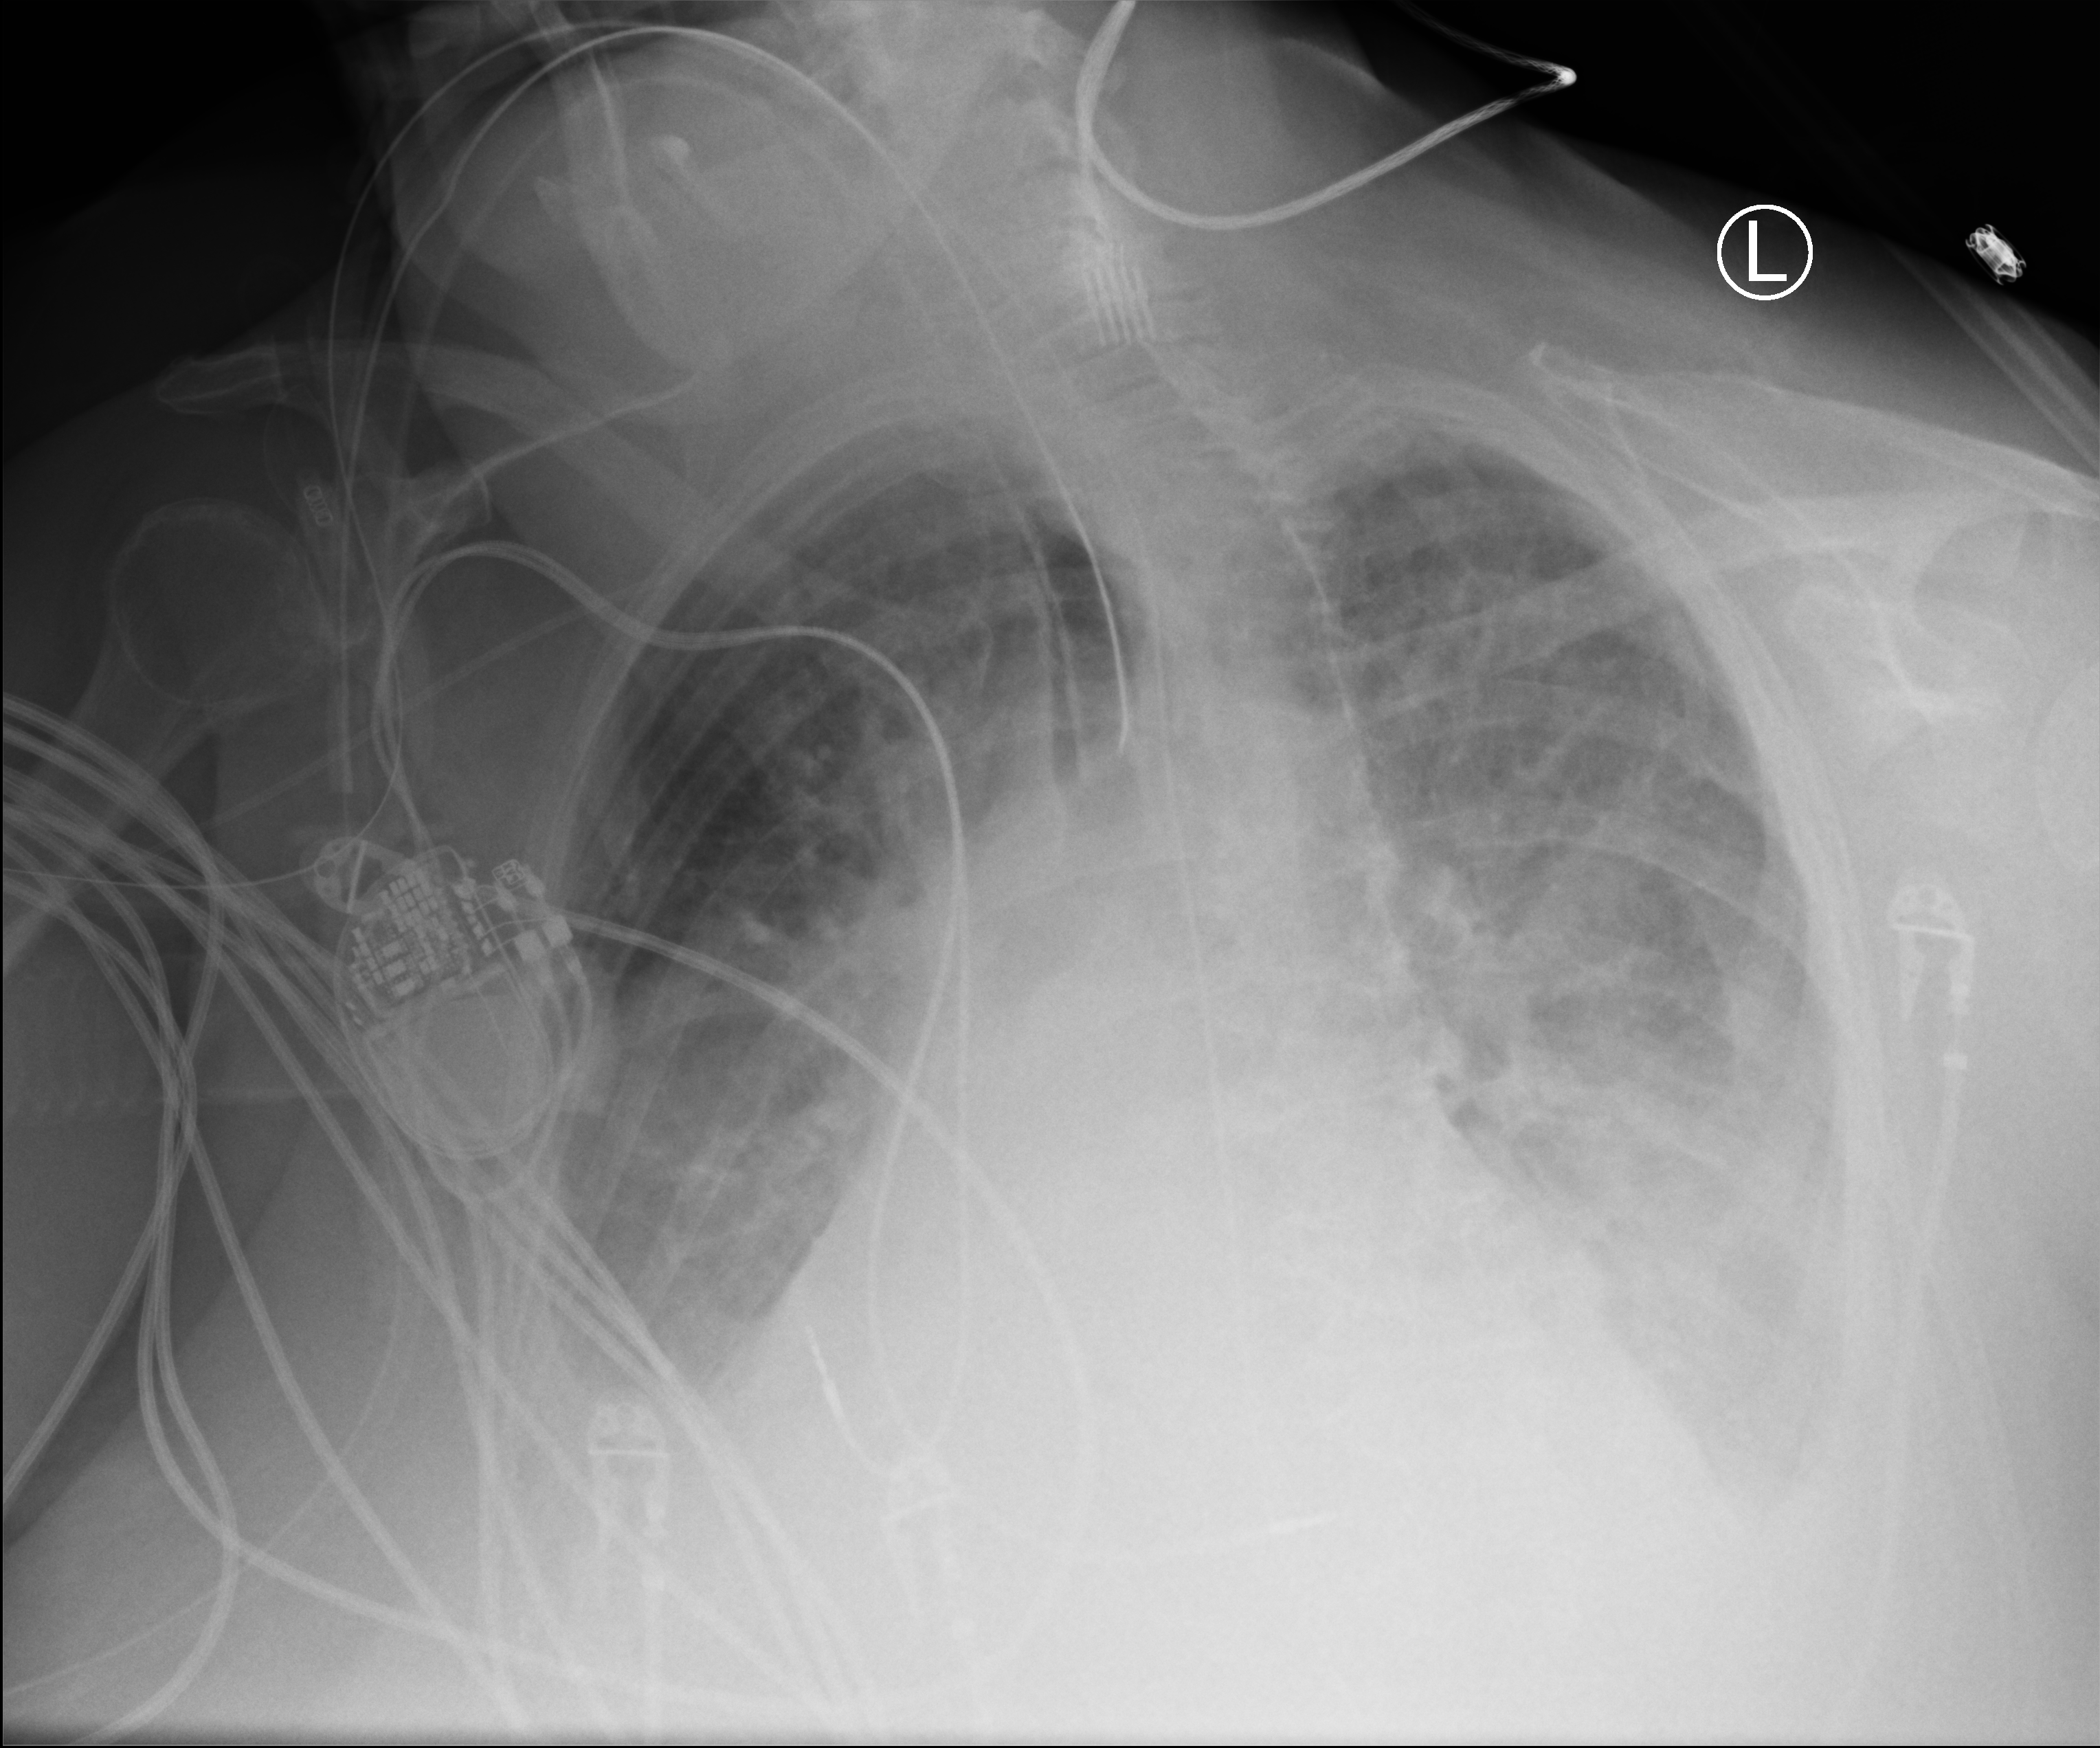
Chest X-ray (portable), anteroposterior (AP) projection. Female patient hospitalised with COVID-19, age 75–90 years.
From the hospital-stay record, not from the radiograph (when in the stay this image was taken is not recorded): admitted to intensive care during this hospital stay: yes; mechanically ventilated during this hospital stay: yes; hypertension (admission record): yes.